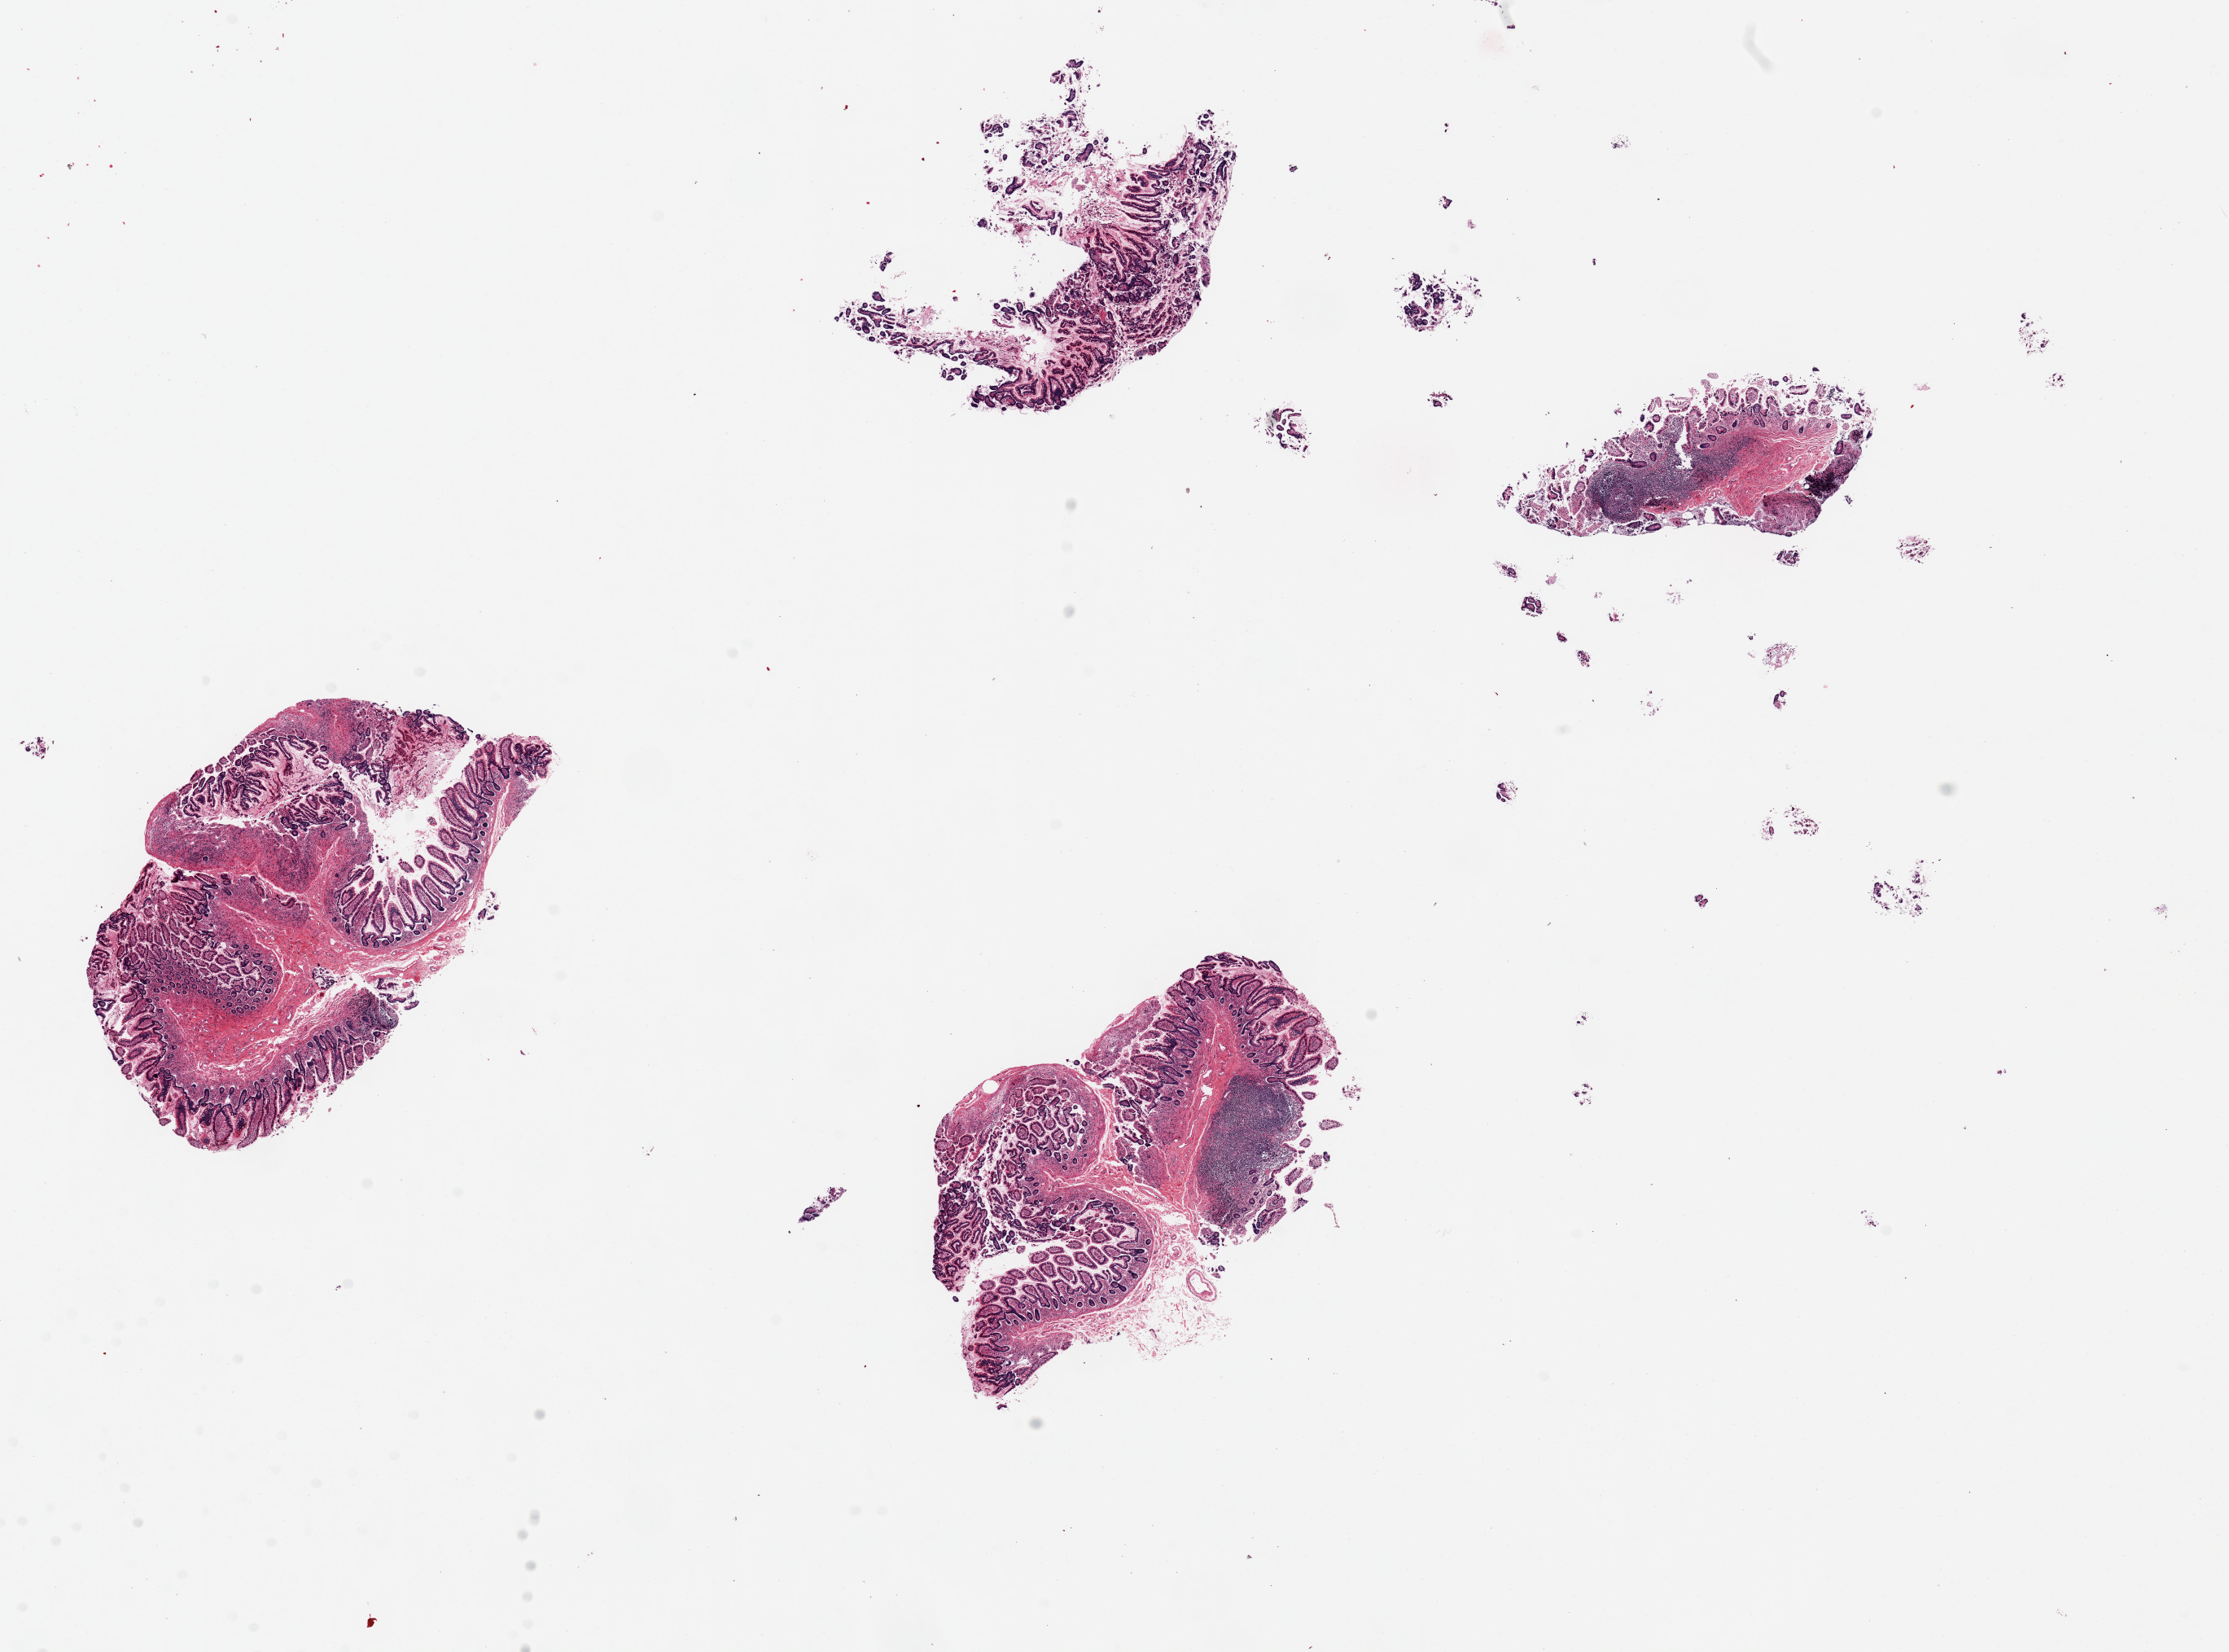
Digitized H&E-stained section, whole scanned area (about 21.7 x 16.0 mm, slide scanned at 20x) shown as a low-resolution overview; PAXgene-fixed, paraffin-embedded tissue; target tissue: ileum; tissue donor sample. Donor: male.
Reviewer comment on this tissue sample: 4 pieces ~20% lymphoid elements, rest mainly mucosa ~4x2mm.